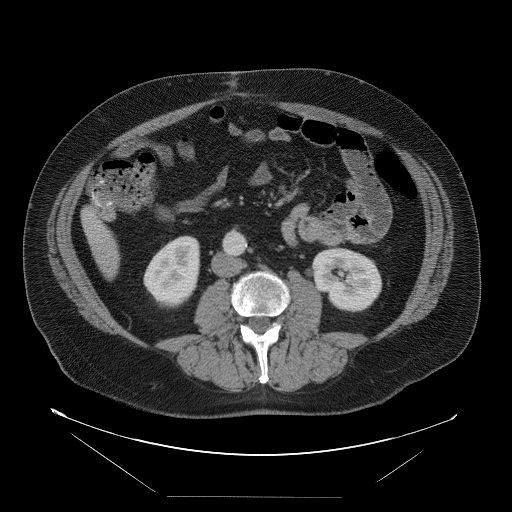
Contrast-enhanced abdominal CT, one axial slice. Slice 16 of 114 in the series (ordered by position). Intravenous contrast given. Soft-tissue window (W 400 / L 40 HU). 5 mm slice thickness. 512 × 512 image matrix, field of view 500 × 500 mm. Male patient, age 61 years. From the clinical record (not read from this slice): diagnosis: colorectal cancer liver metastases, imaged before liver resection; multiple liver metastases: no; largest metastasis: 6.5 cm.
Structures marked on this image (expert manual segmentation):
- liver: bounding box [x1, y1, x2, y2] px = [83, 208, 120, 277]